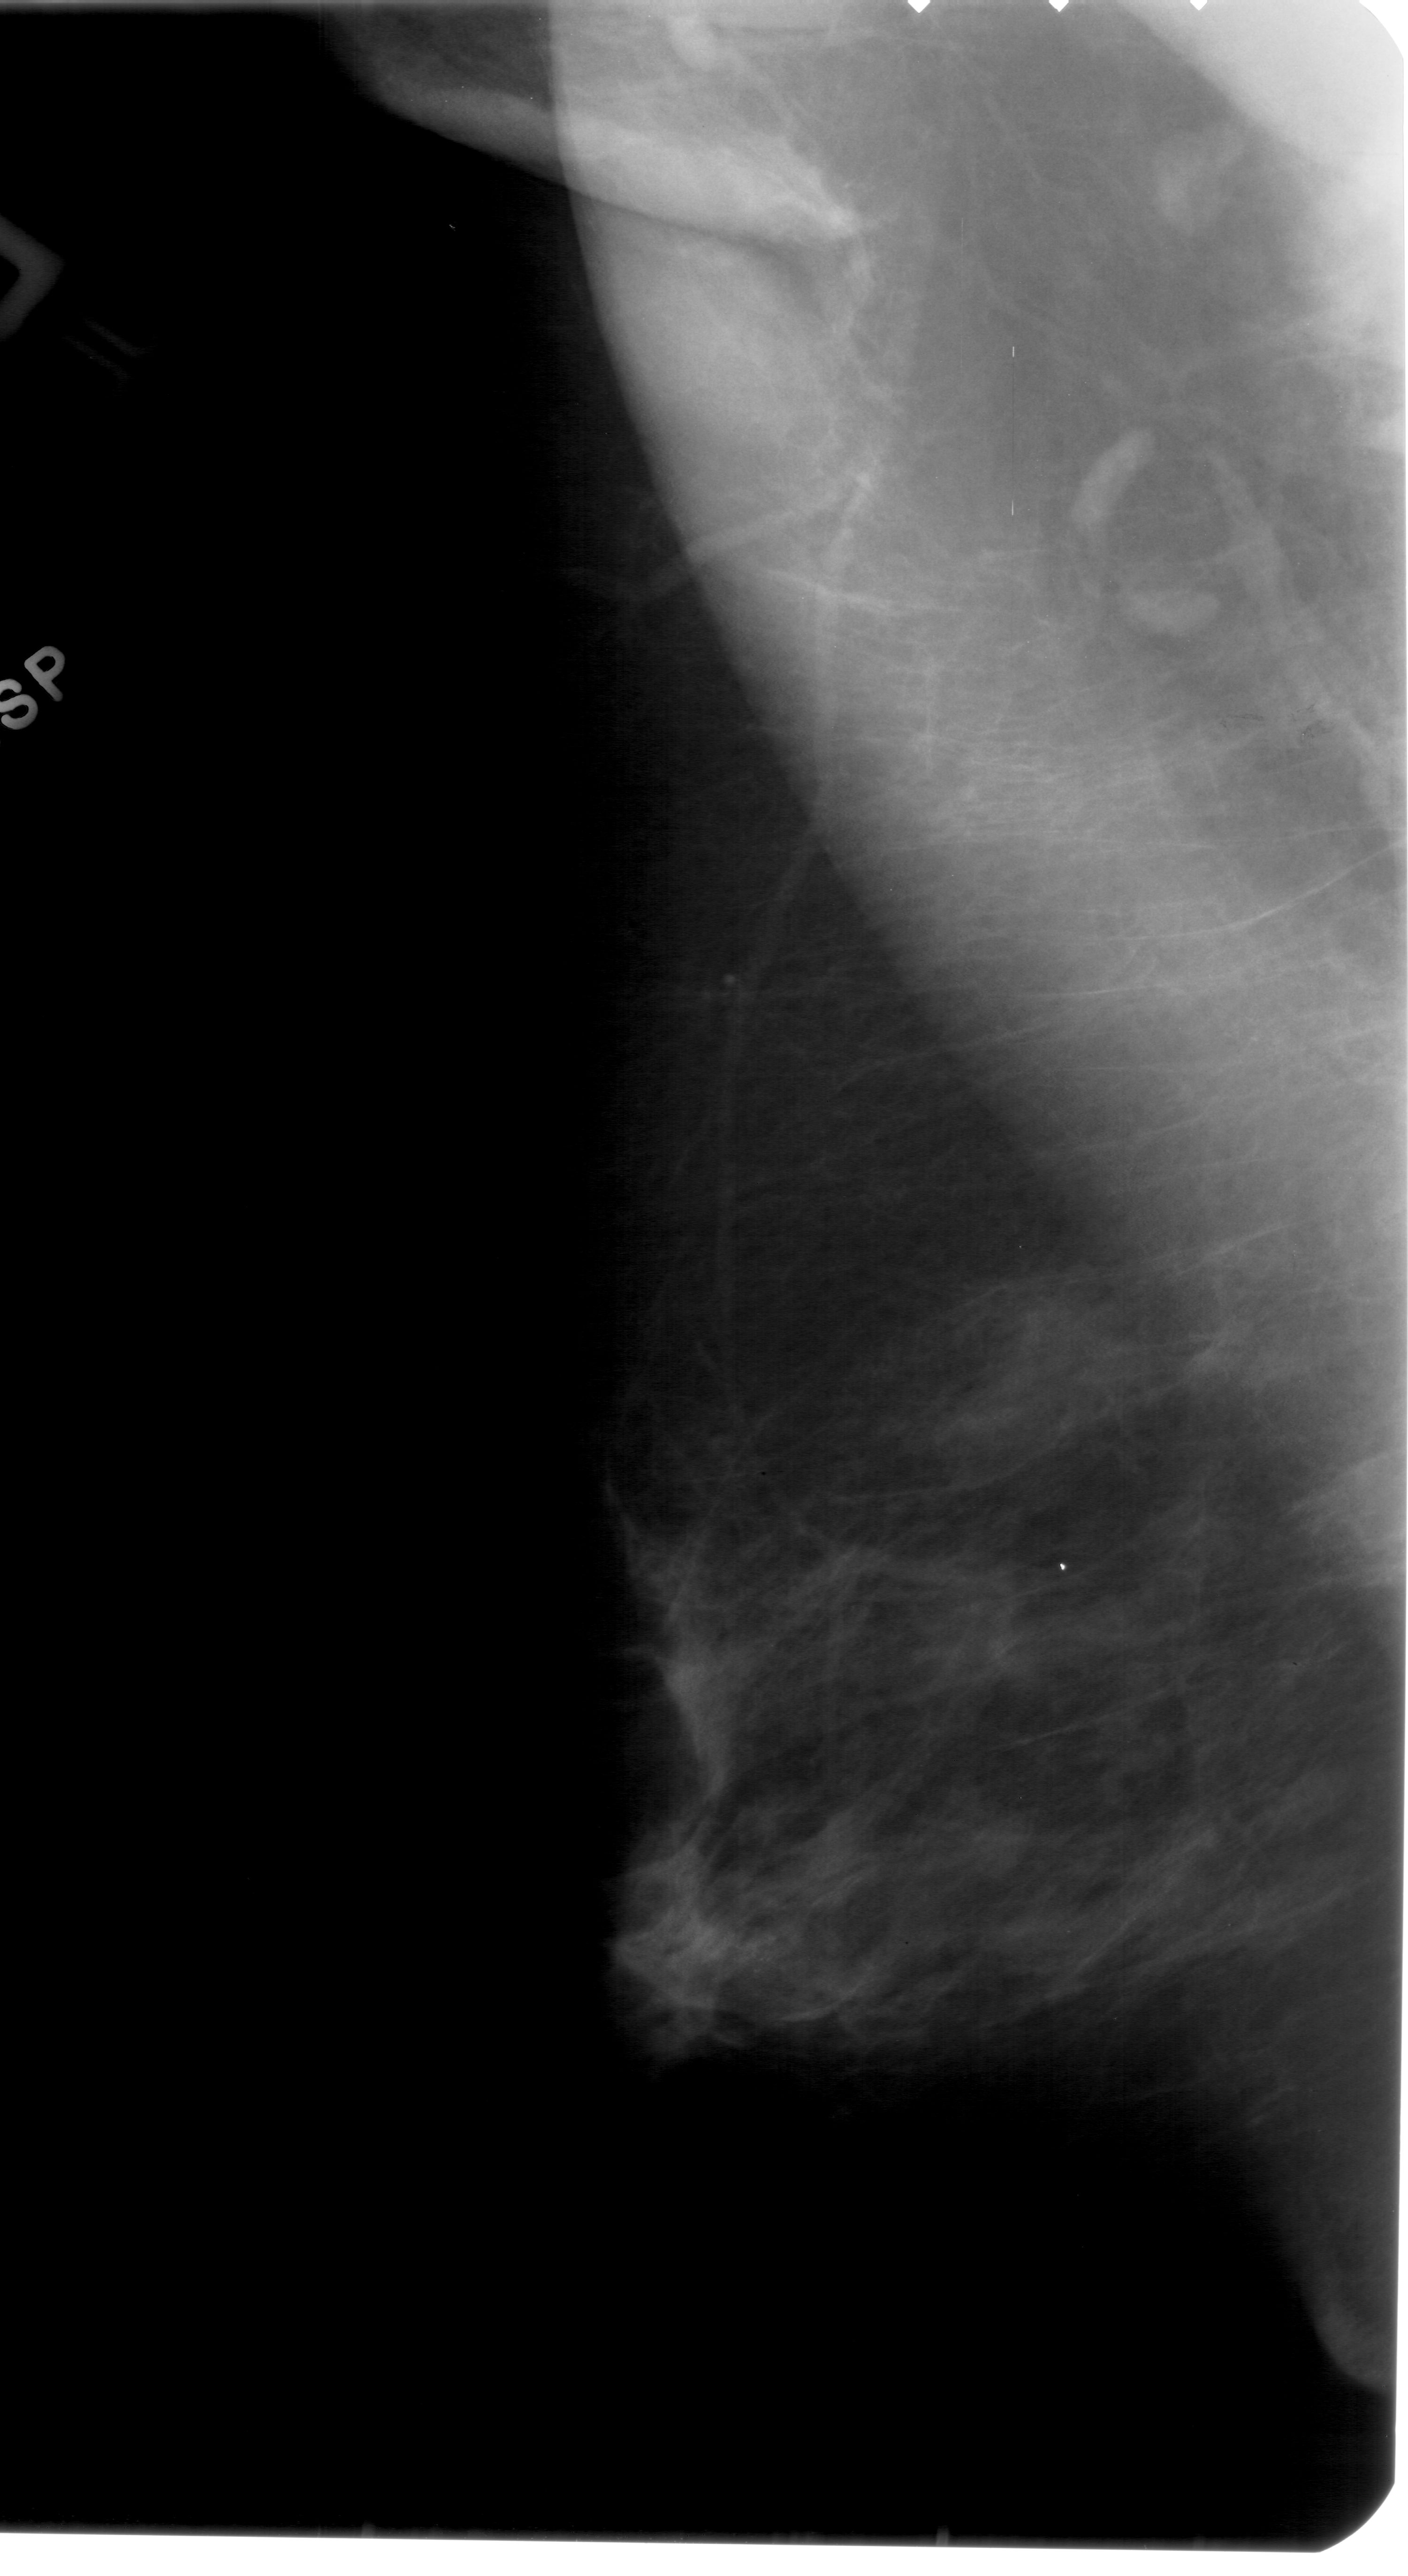
Digitized screen-film mammogram, left breast, MLO view, breast composition: scattered fibroglandular densities (BI-RADS density category 2 of 4).
Abnormality record for this image: calcifications, morphology pleomorphic, distribution clustered; BI-RADS assessment category 4; pathology result (as recorded, not read from the image): benign.